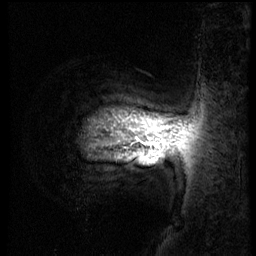
Breast MRI (dynamic contrast-enhanced), one sagittal slice. Slice 50 of 56 in the series (ordered by position). 3 images stored at this slice position (order not interpretable as contrast timing). 1.5 T. TE 4.2 ms, TR 8.9 ms. 256 × 256 image matrix, field of view 220 × 220 mm. Female patient, age 57 years. Case-level facts recorded for this patient, not image findings: setting: breast cancer imaged before/during neoadjuvant chemotherapy; receptor status: HER2-positive.
Annotated regions visible in this slice (semi-automatically segmented with operator editing):
- analysis volume of interest (the breast-tissue region the enhancement analysis was run in; not a lesion): bounding box [x1, y1, x2, y2] px = [81, 70, 228, 156]
- tumour enhancement mask (voxels above the 140 % enhancement threshold inside the analysis volume of interest): [149, 151, 151, 153]